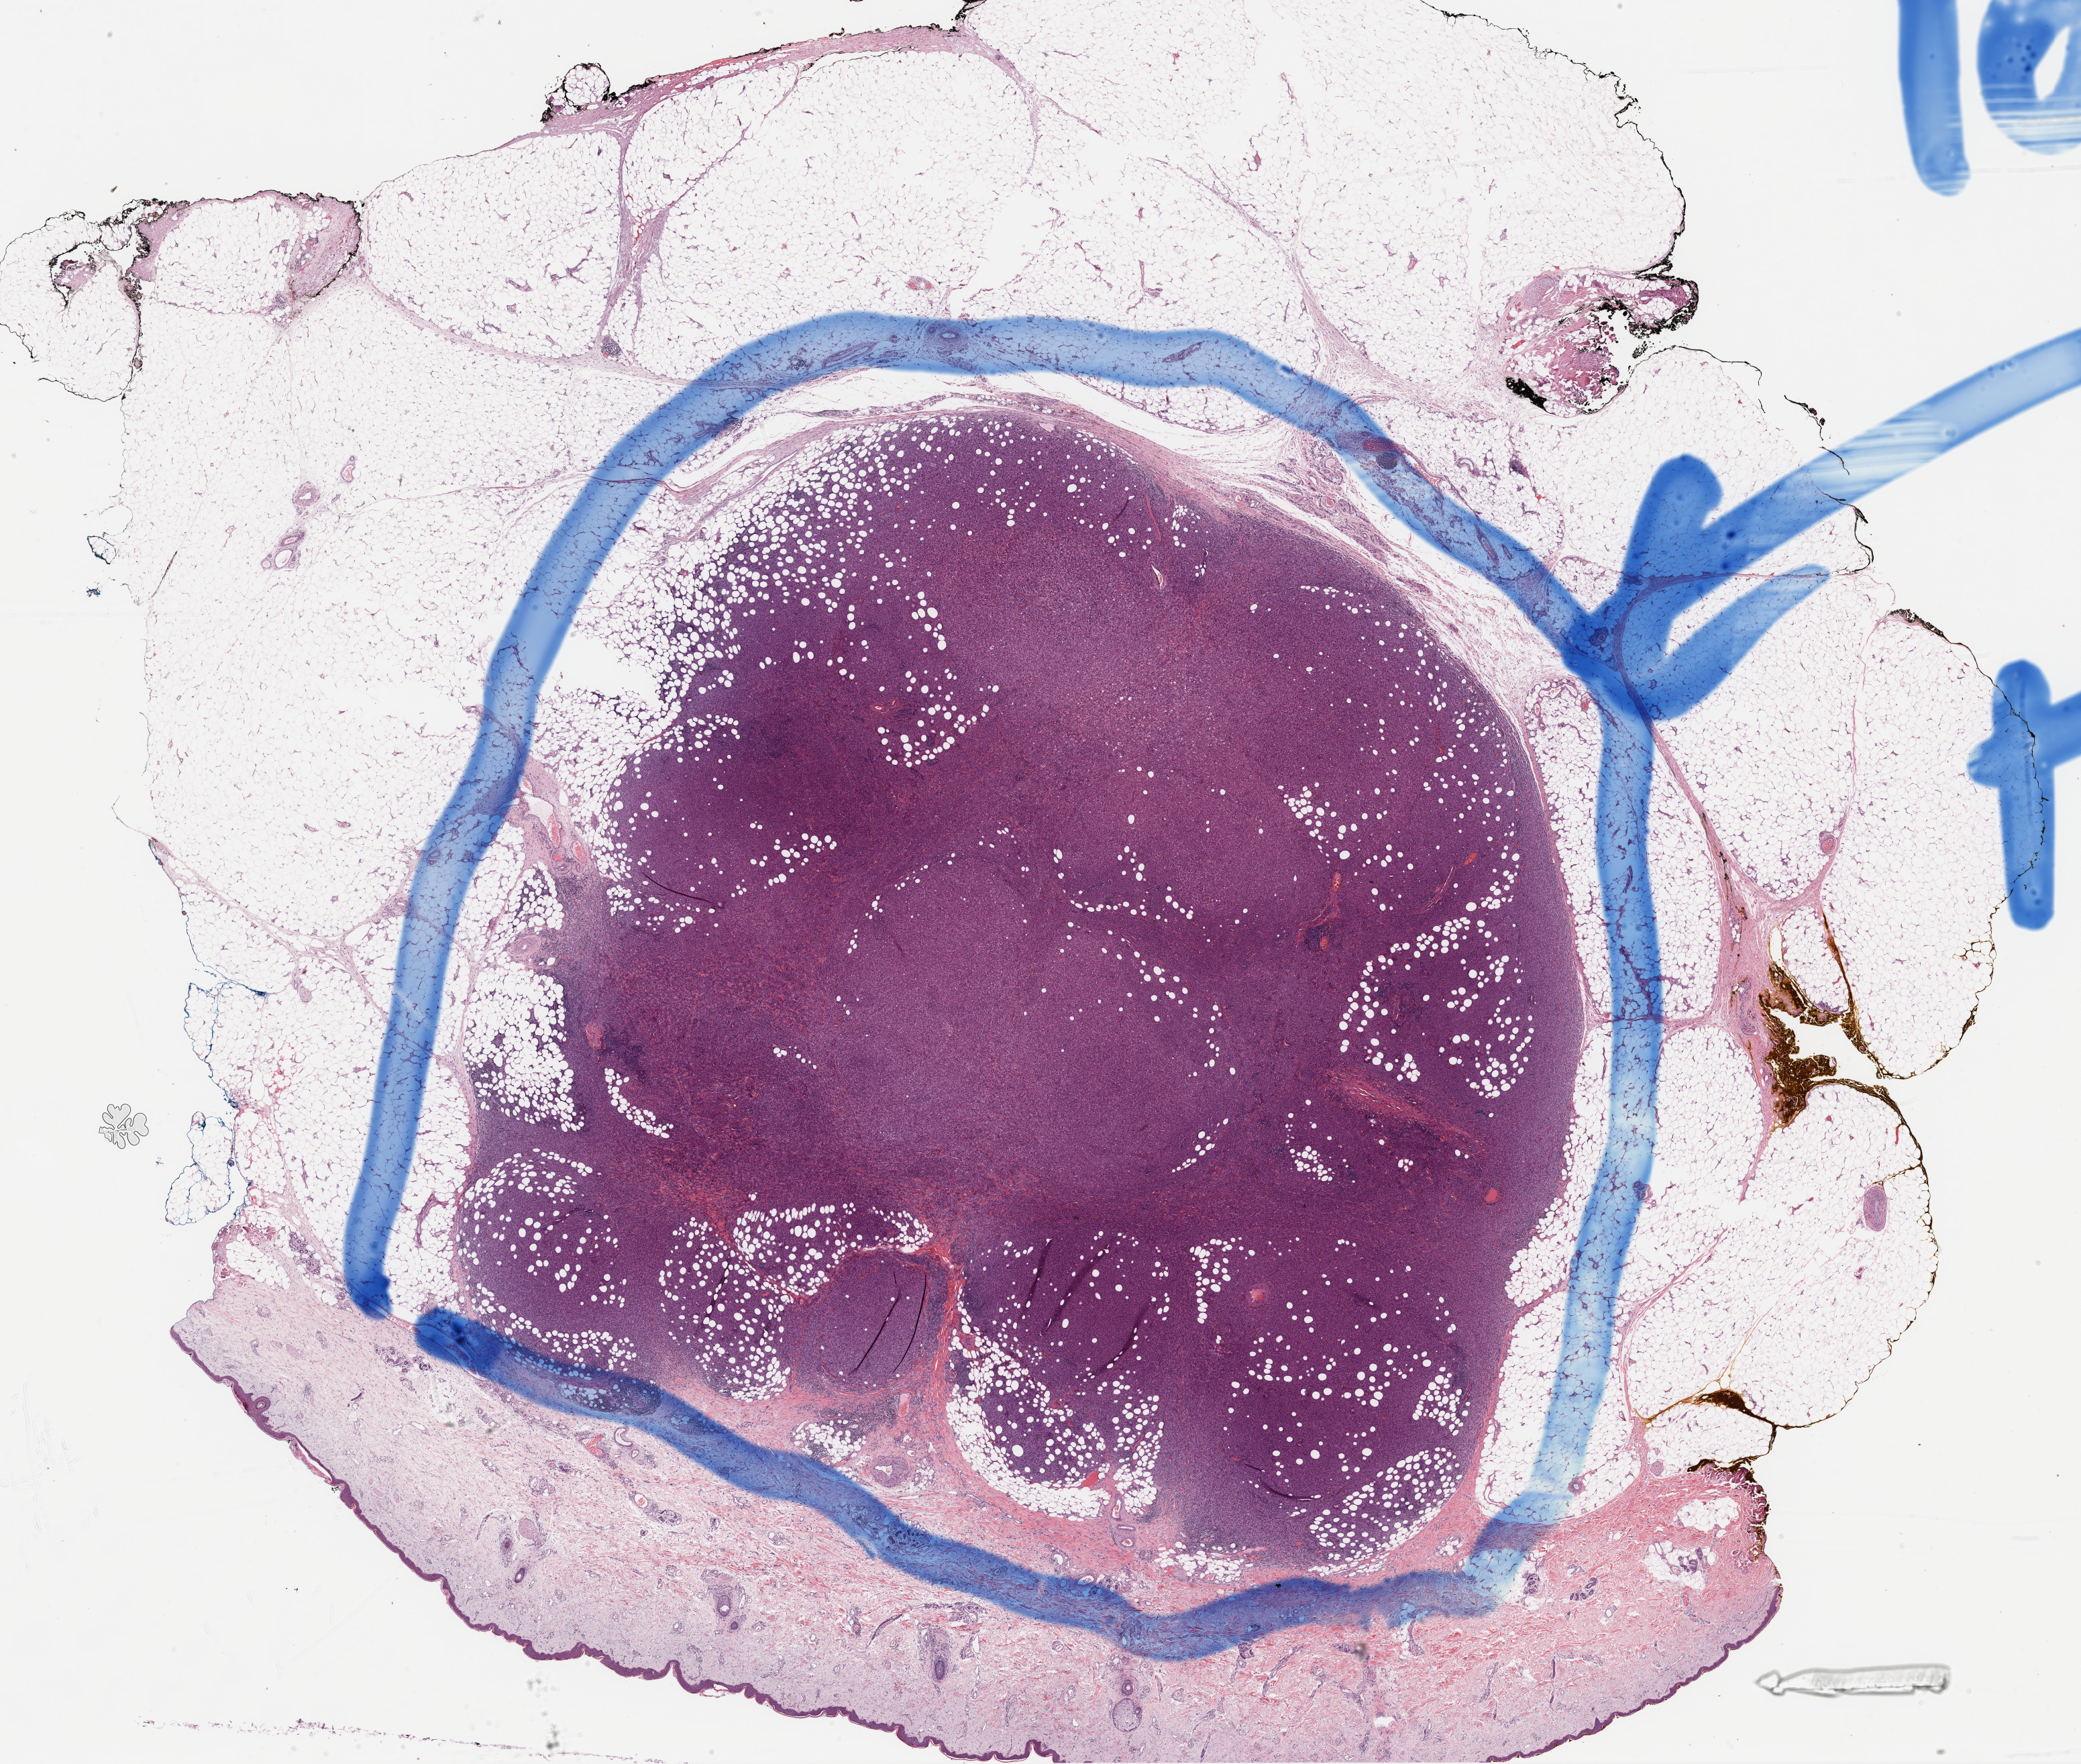
Whole-slide histology image, H&E-stained, a low-resolution overview of the entire scanned area, about 25.0 x 21.2 mm. Formalin-fixed paraffin-embedded (FFPE) diagnostic section. Metastatic tumour sample. Patient: male, age at initial diagnosis 74 years.
This section: metastatic tumour tissue. Patient diagnosis: Malignant melanoma, NOS.